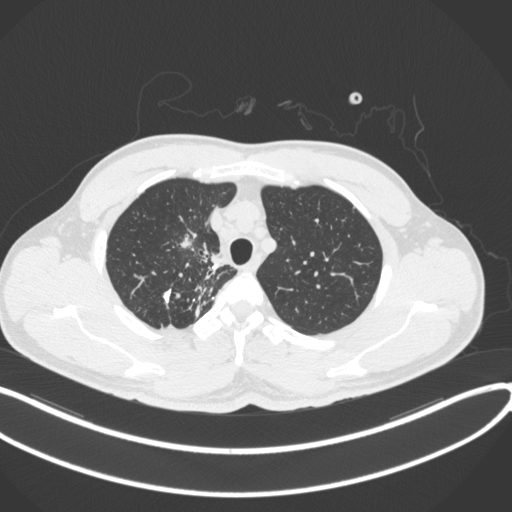
Chest CT, one axial slice; slice 302 of 391 in the series (ordered by position); 120 kVp; lung window (W 1500 / L -600 HU); 1 mm slice thickness; 512 × 512 image matrix, field of view 400 × 400 mm. Male patient, age 48 years. From the clinical record (not read from this slice): clinical TNM (as recorded): T1c N1 M1.
Structures marked on this image (bounding box drawn by a radiologist):
- lung tumour (recorded histology: adenocarcinoma): bounding box [x1, y1, x2, y2] px = [170, 225, 203, 253]